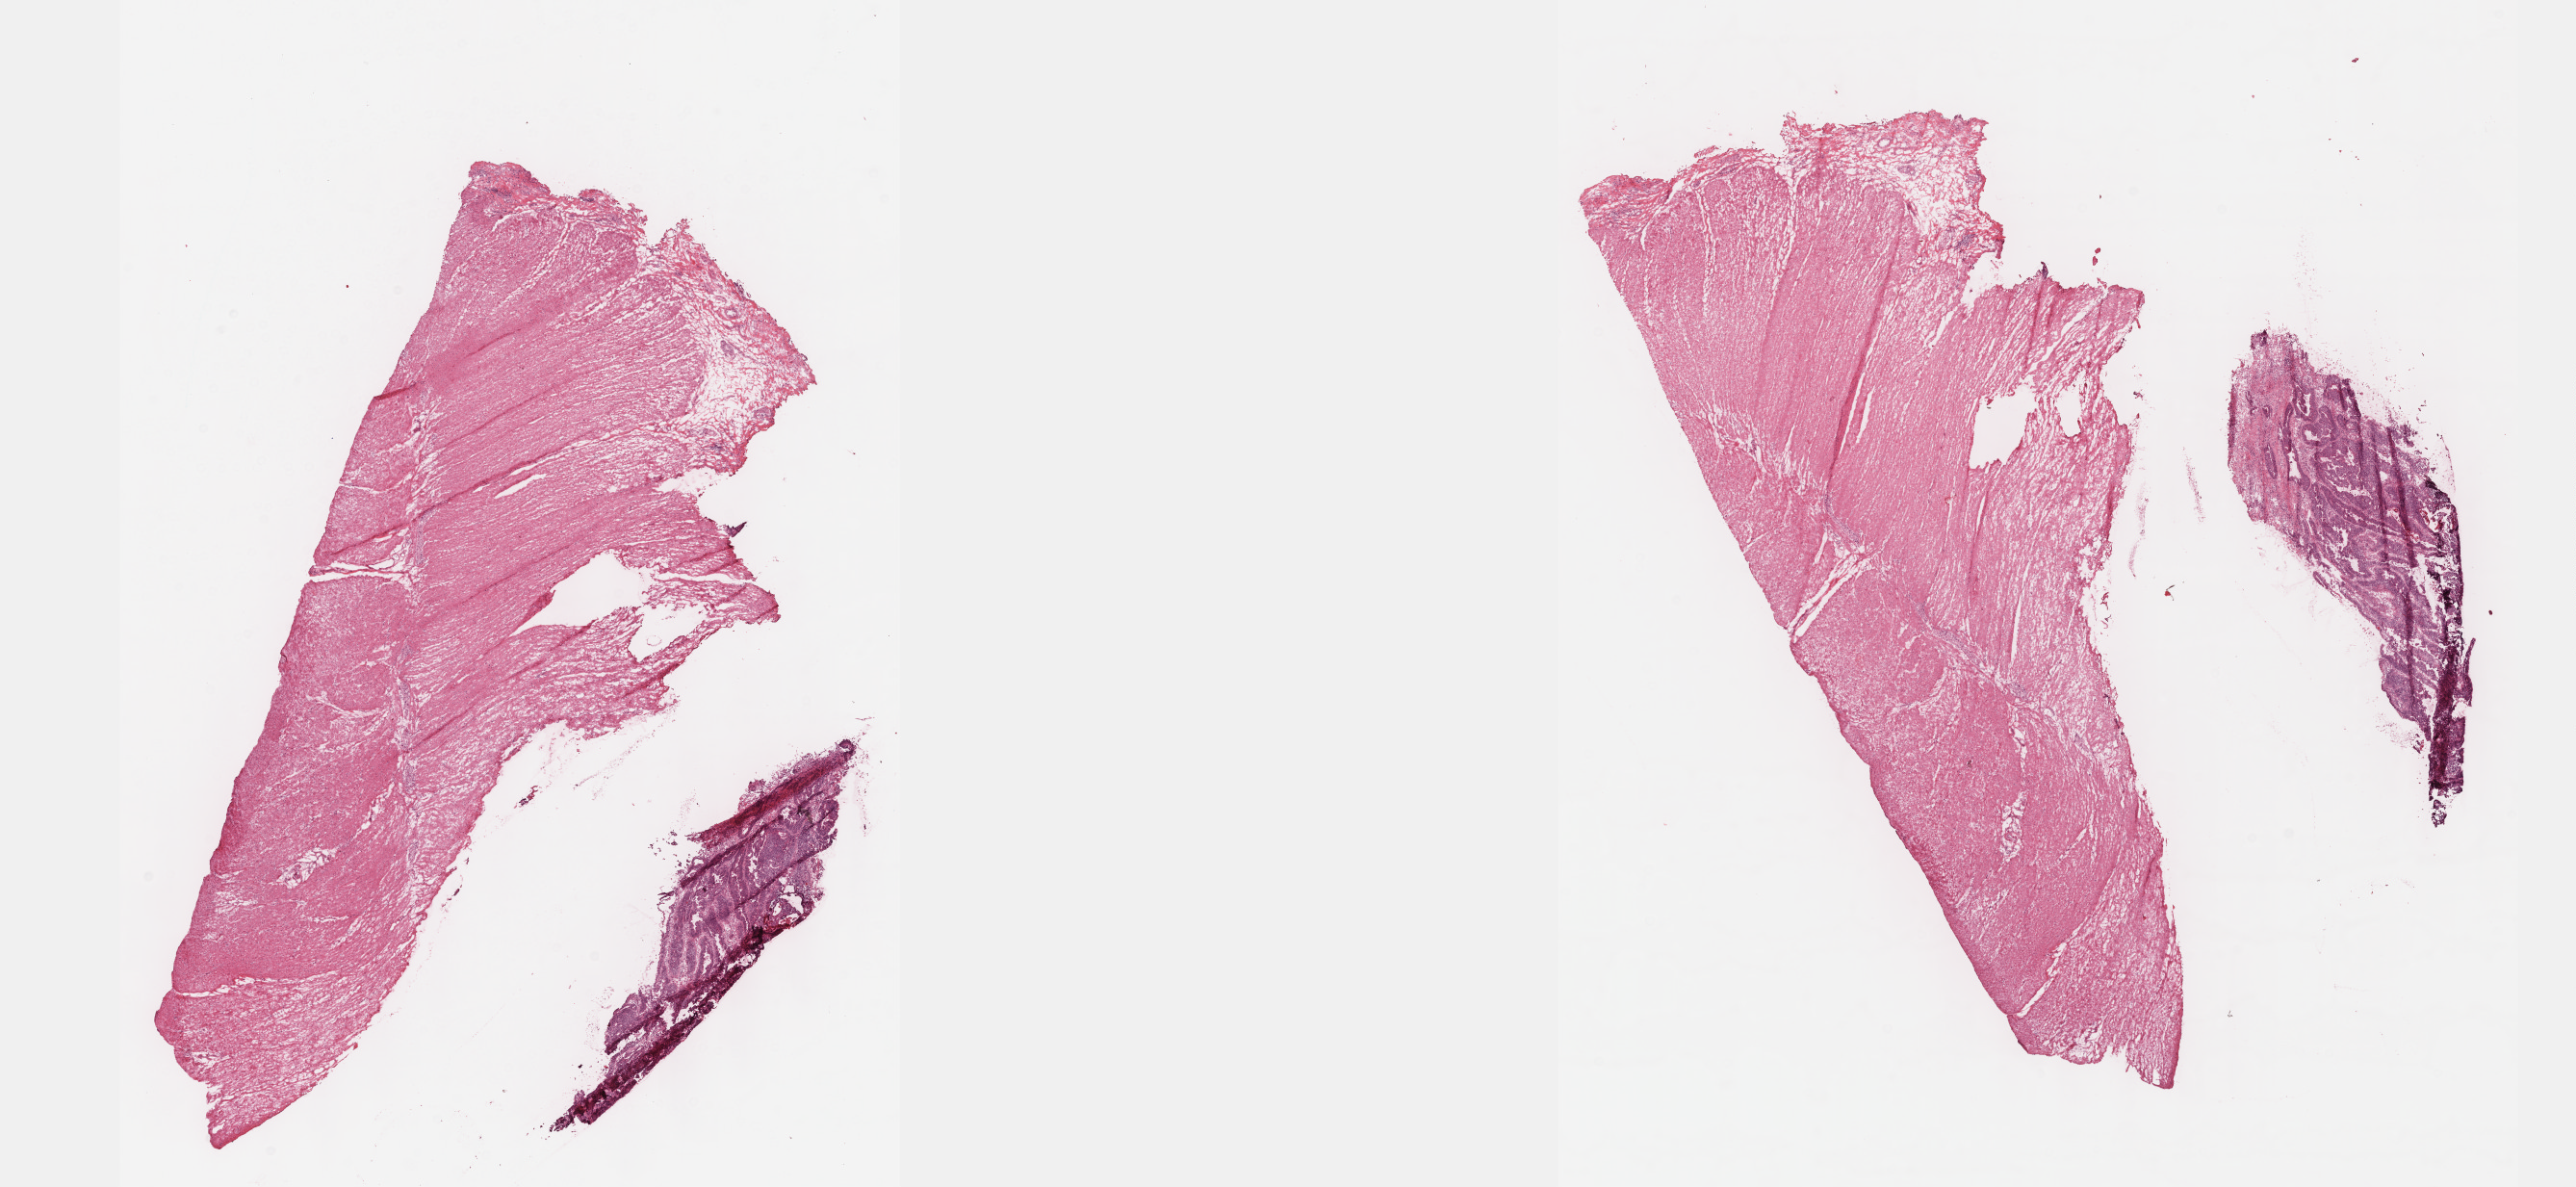
Hematoxylin and eosin (H&E) stained whole-slide image, low-resolution overview of the scanned area, about 21.6 x 10.0 mm; frozen section from the top of the tissue portion; primary tumour sample from the rectum. Male, age 66 years at initial diagnosis. Slide review estimates, as recorded: tumour cells 10%, tumour nuclei 20%, normal cells 89%, stromal cells 0%, necrosis 1%. Inflammatory infiltration, as recorded: lymphocyte infiltration 5%, monocyte infiltration 0%, neutrophil infiltration 0%.
AJCC pathologic stage: II (5th edition). Histologic diagnosis: Adenocarcinoma, NOS.